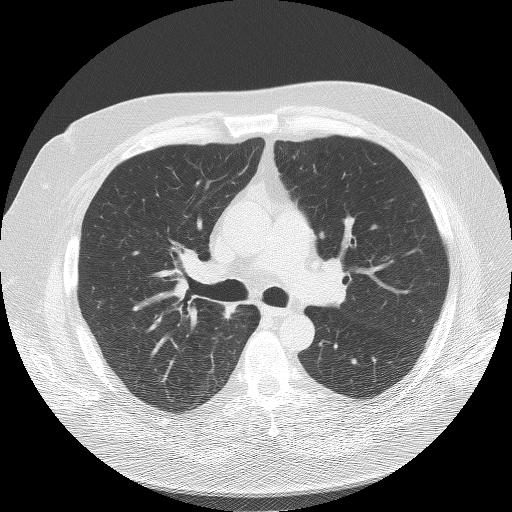
Chest CT (low-dose screening protocol), one axial image; third screening round (two years after baseline); lung window (W 1500 / L -600 HU); lung (sharp) reconstruction kernel (BONE); 512 × 512 image matrix, field of view 360 × 360 mm. Male participant, aged 58 years at enrolment. Former smoker at enrolment.
• Lesion marked by an expert reader, bounding box <194,288,256,339> (left, top, right, bottom; pixels).
• The exam's reader record, not a measurement of the box and not confirmed to be the same lesion: non-calcified nodule or mass ≥4 mm, right upper lobe, 9 × 8 mm, spiculated (stellate) margins, soft tissue attenuation, pre-existing on the prior screen: yes; interval growth: yes.
• Lung cancer was diagnosed 157 days after this screen: squamous cell carcinoma, NOS, right upper lobe, moderately differentiated (G2), stage IA (AJCC 6th edition), 18 mm at pathology.